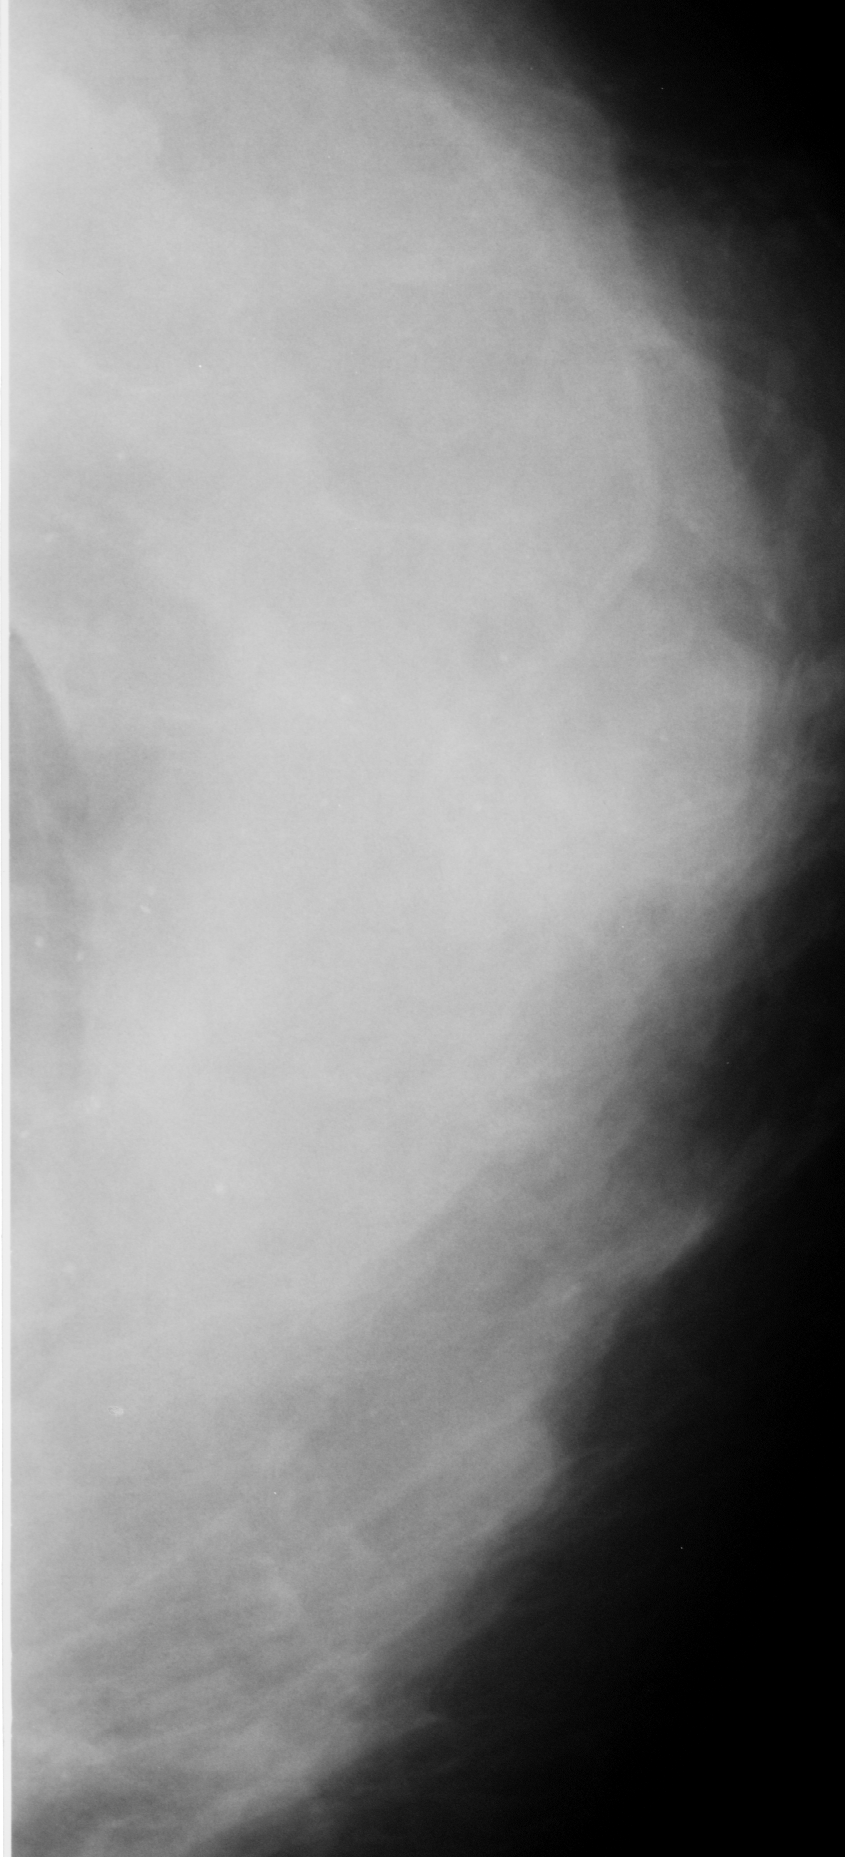
Cropped region of a digitized screen-film mammogram centred on a radiologist-marked abnormality, left breast, CC view.
Finding: calcifications, morphology punctate, distribution diffusely scattered; BI-RADS assessment category 2; subtlety rating 4 on a 1 (subtle) to 5 (obvious) scale; pathology result (as recorded, not read from the image): benign.